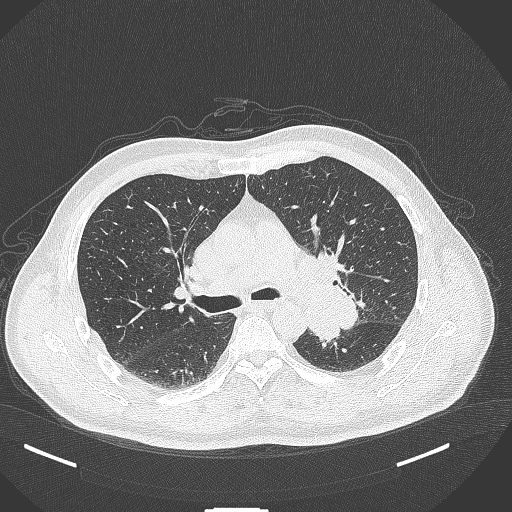
Chest CT, one axial slice; position 259 of 429 along the scan axis; reconstruction kernel B70f; 120 kVp; lung window (W 1500 / L -600 HU); 1 mm slice thickness; 512 × 512 image matrix, field of view 400 × 400 mm. Patient: male, 55 years. From the clinical record (not read from this slice): clinical TNM (as recorded): T3 N0 M1c.
Annotated regions visible in this slice (rectangle marked by the reading radiologist):
- lung tumour (recorded histology: adenocarcinoma): box from (x=305, y=284) to (x=365, y=348) px